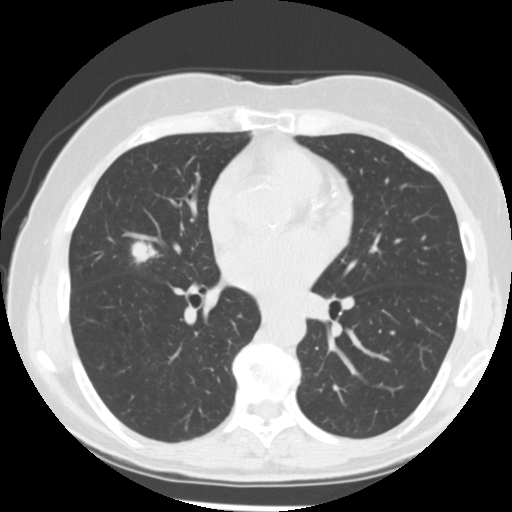
Low-dose screening chest CT, one axial slice; position 136 of 255 along the scan axis; reconstruction kernel STANDARD; 120 kVp; lung window (W 1500 / L -600 HU); 2.5 mm slice thickness; 512 × 512 image matrix, field of view 320 × 320 mm.
Structures marked on this image (expert manual segmentation):
- lesion 1 (tumor, middle lobe of right lung): box from (x=131, y=240) to (x=157, y=264) px